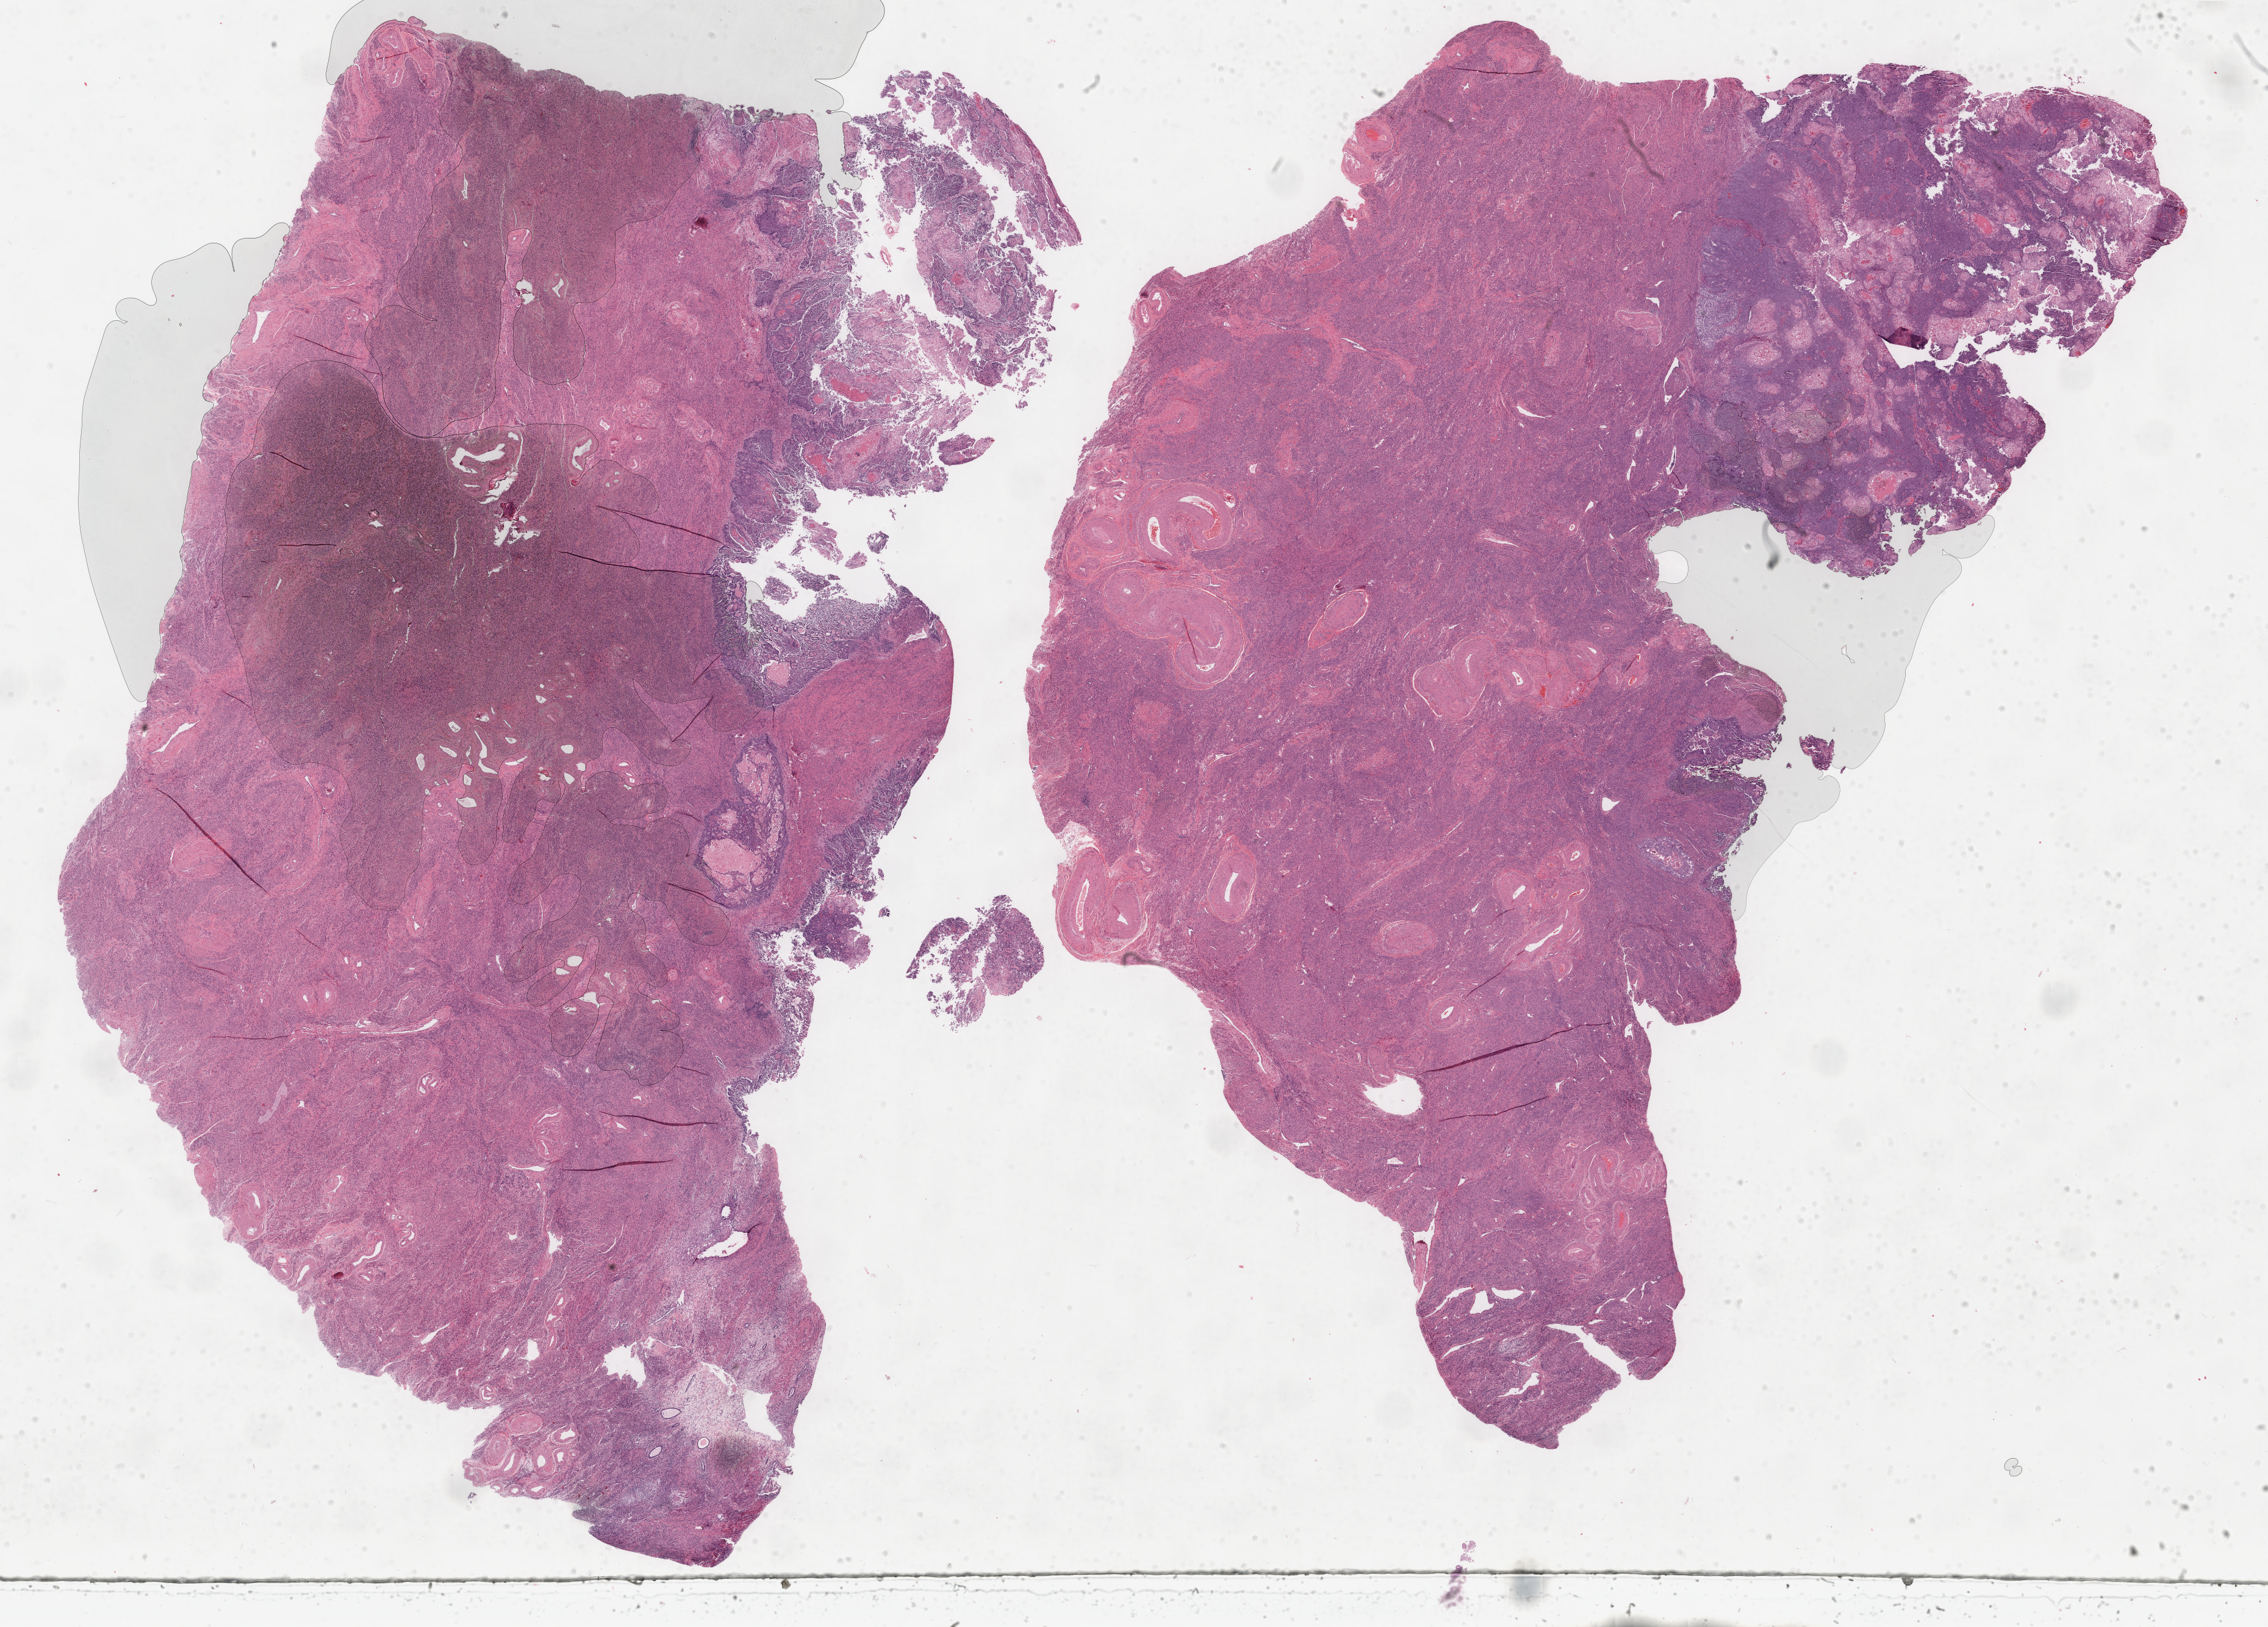
Whole-slide histology image, H&E-stained — a low-resolution overview of the entire scanned area, about 29.5 x 21.2 mm. Formalin-fixed paraffin-embedded (FFPE) diagnostic section. Primary tumour sample from the uterus. Female patient; age at initial diagnosis 67 years. Histologic grade: G3 (poorly differentiated).
• FIGO stage: IB
• diagnosis: Endometrioid adenocarcinoma, NOS